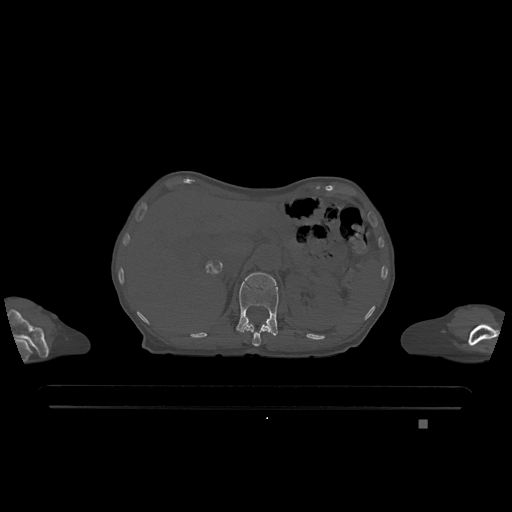
CT including the spine, one axial slice. Position 494 of 1317 along the scan axis. Bone window (W 1800 / L 400 HU). 0.5 mm slice thickness. 512 × 512 image matrix, field of view 500 × 500 mm. Female patient, age 74 years. From the clinical record (not read from this slice): primary cancer: lung.
Annotated regions visible in this slice (semi-automatically segmented with operator editing):
- L1 vertebra: bounding box <237,272,279,336> (left, top, right, bottom; pixels)
- T12 vertebra: <241,323,270,346>